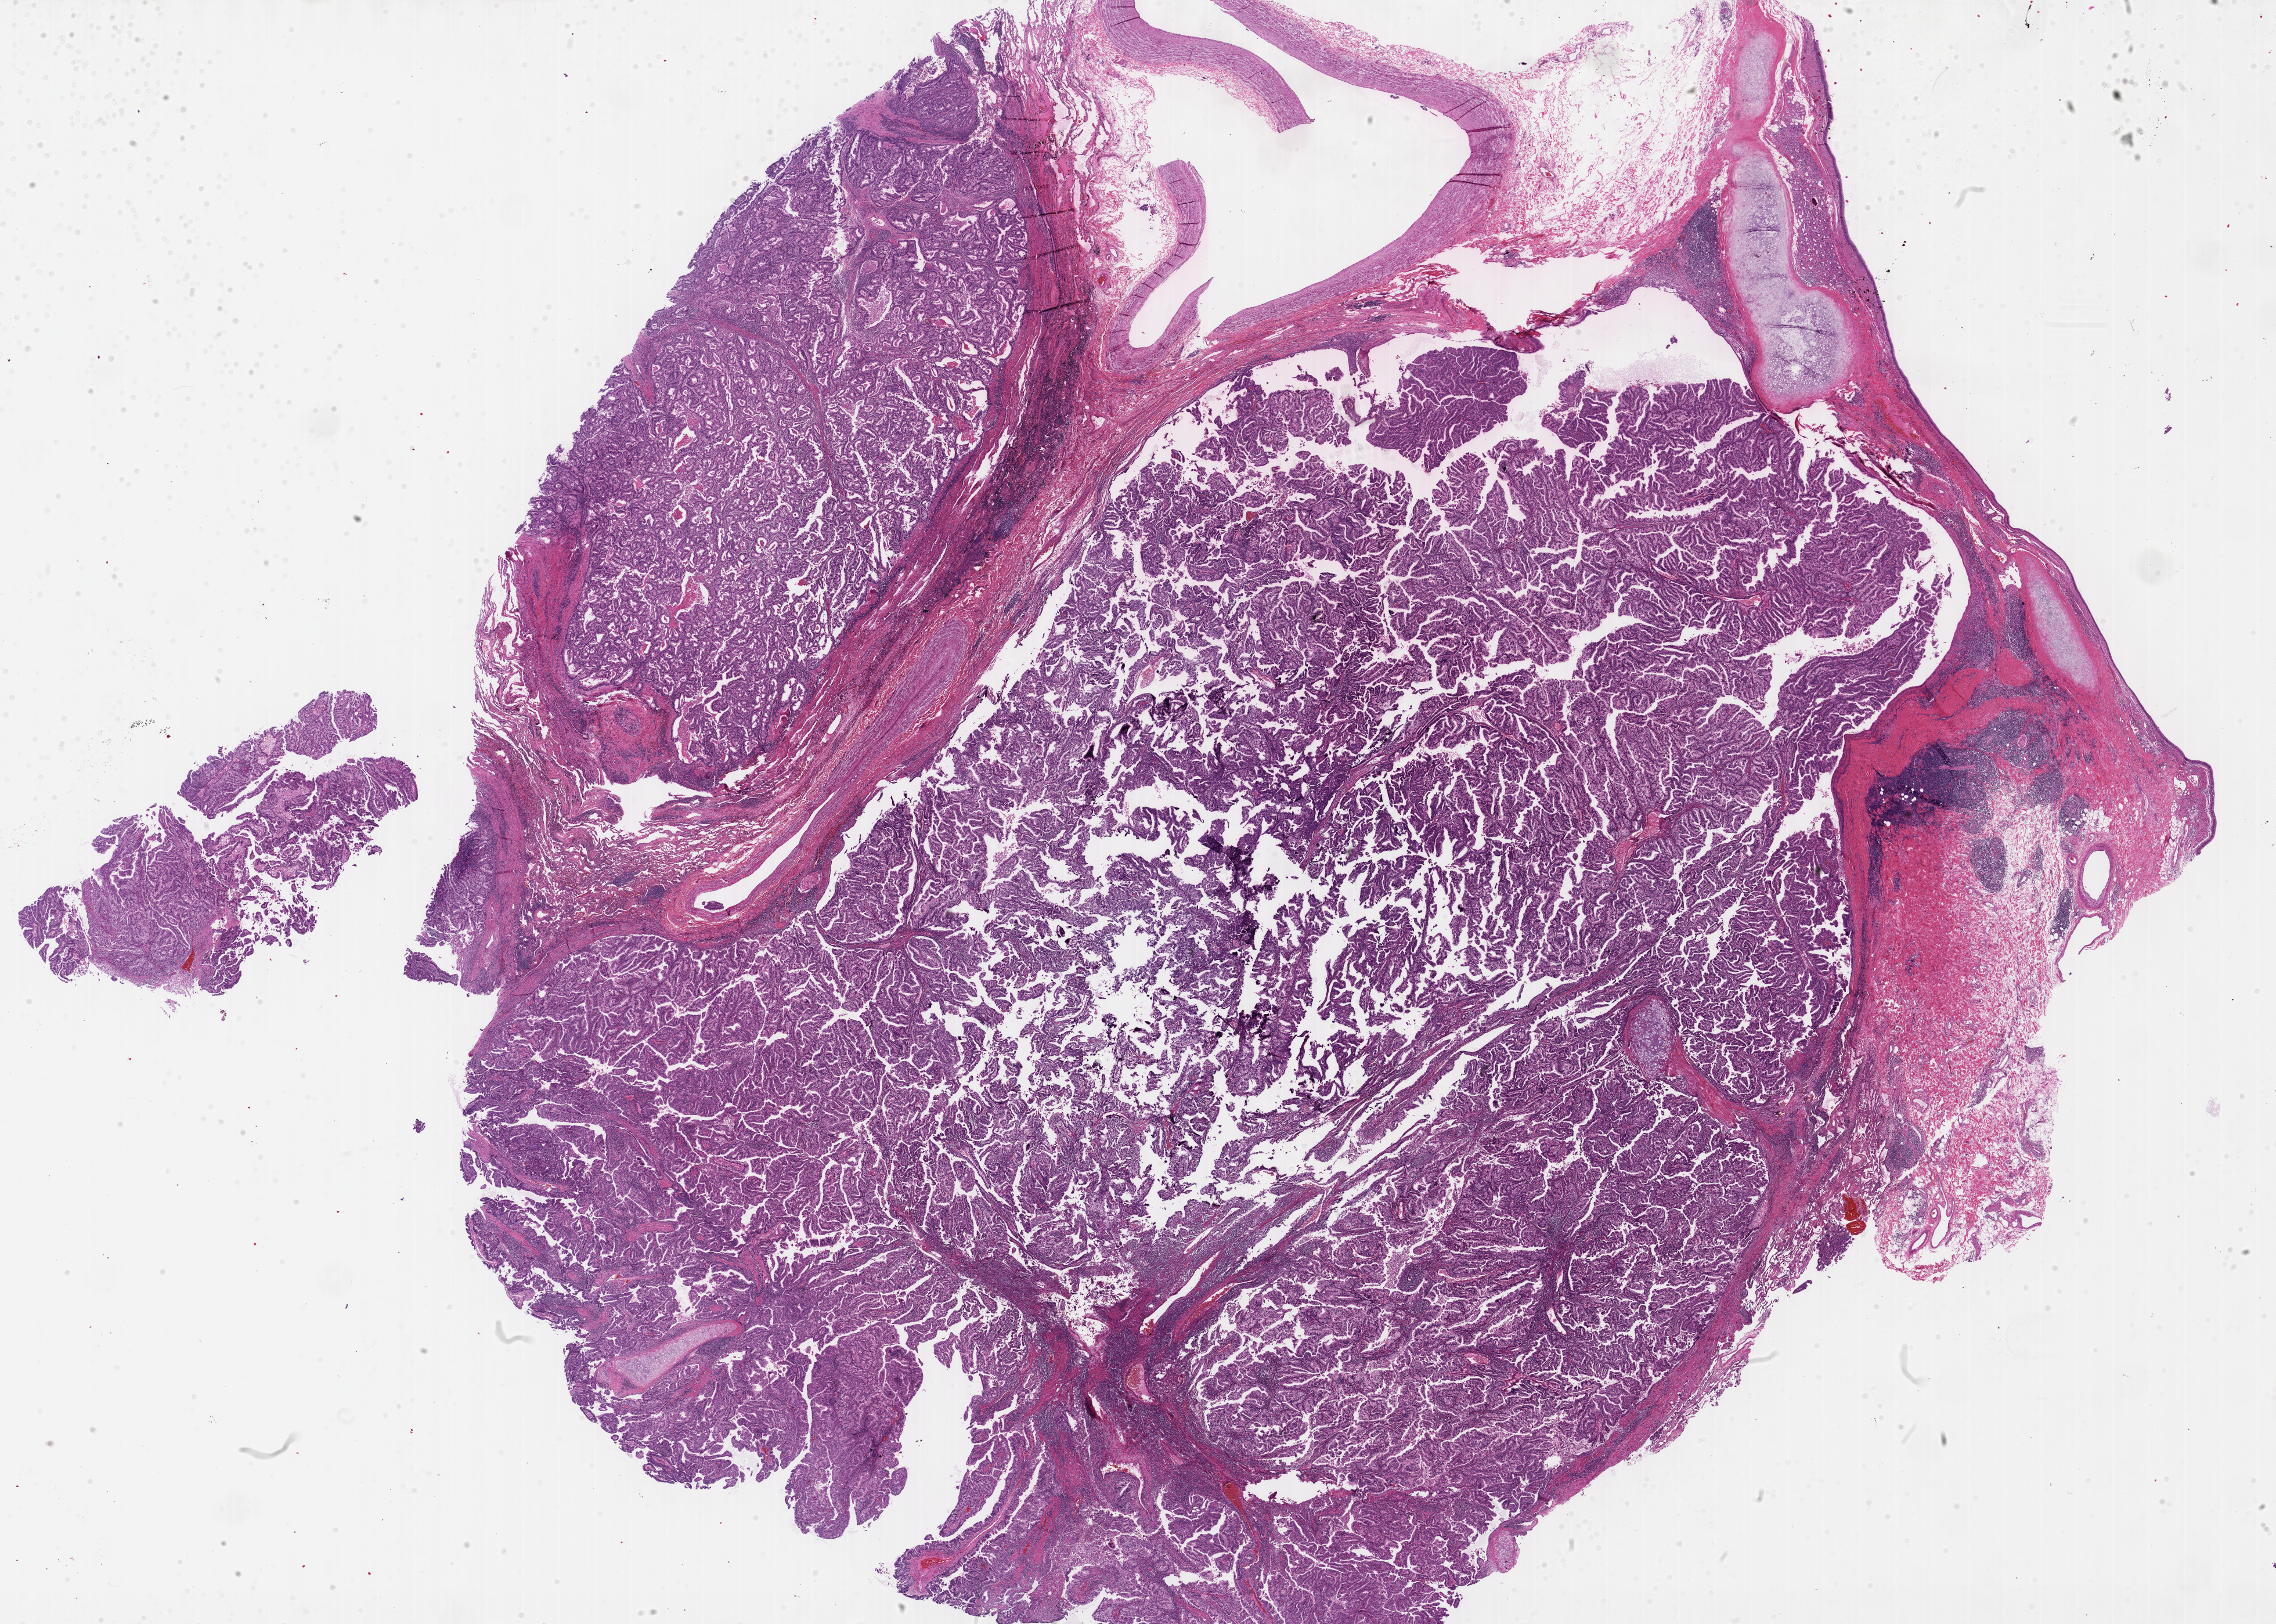
Whole-slide histology image, H&E — whole scanned area (about 31.7 x 22.6 mm, slide scanned at 40x) shown as a low-resolution overview; formalin-fixed paraffin-embedded (FFPE) diagnostic section; primary tumour sample from the lung. Patient: male, age at initial diagnosis 64 years.
AJCC pathologic stage: IB (6th edition). TNM: T2 N0 MX. Histologic diagnosis: Acinar cell carcinoma (lower lobe, lung).